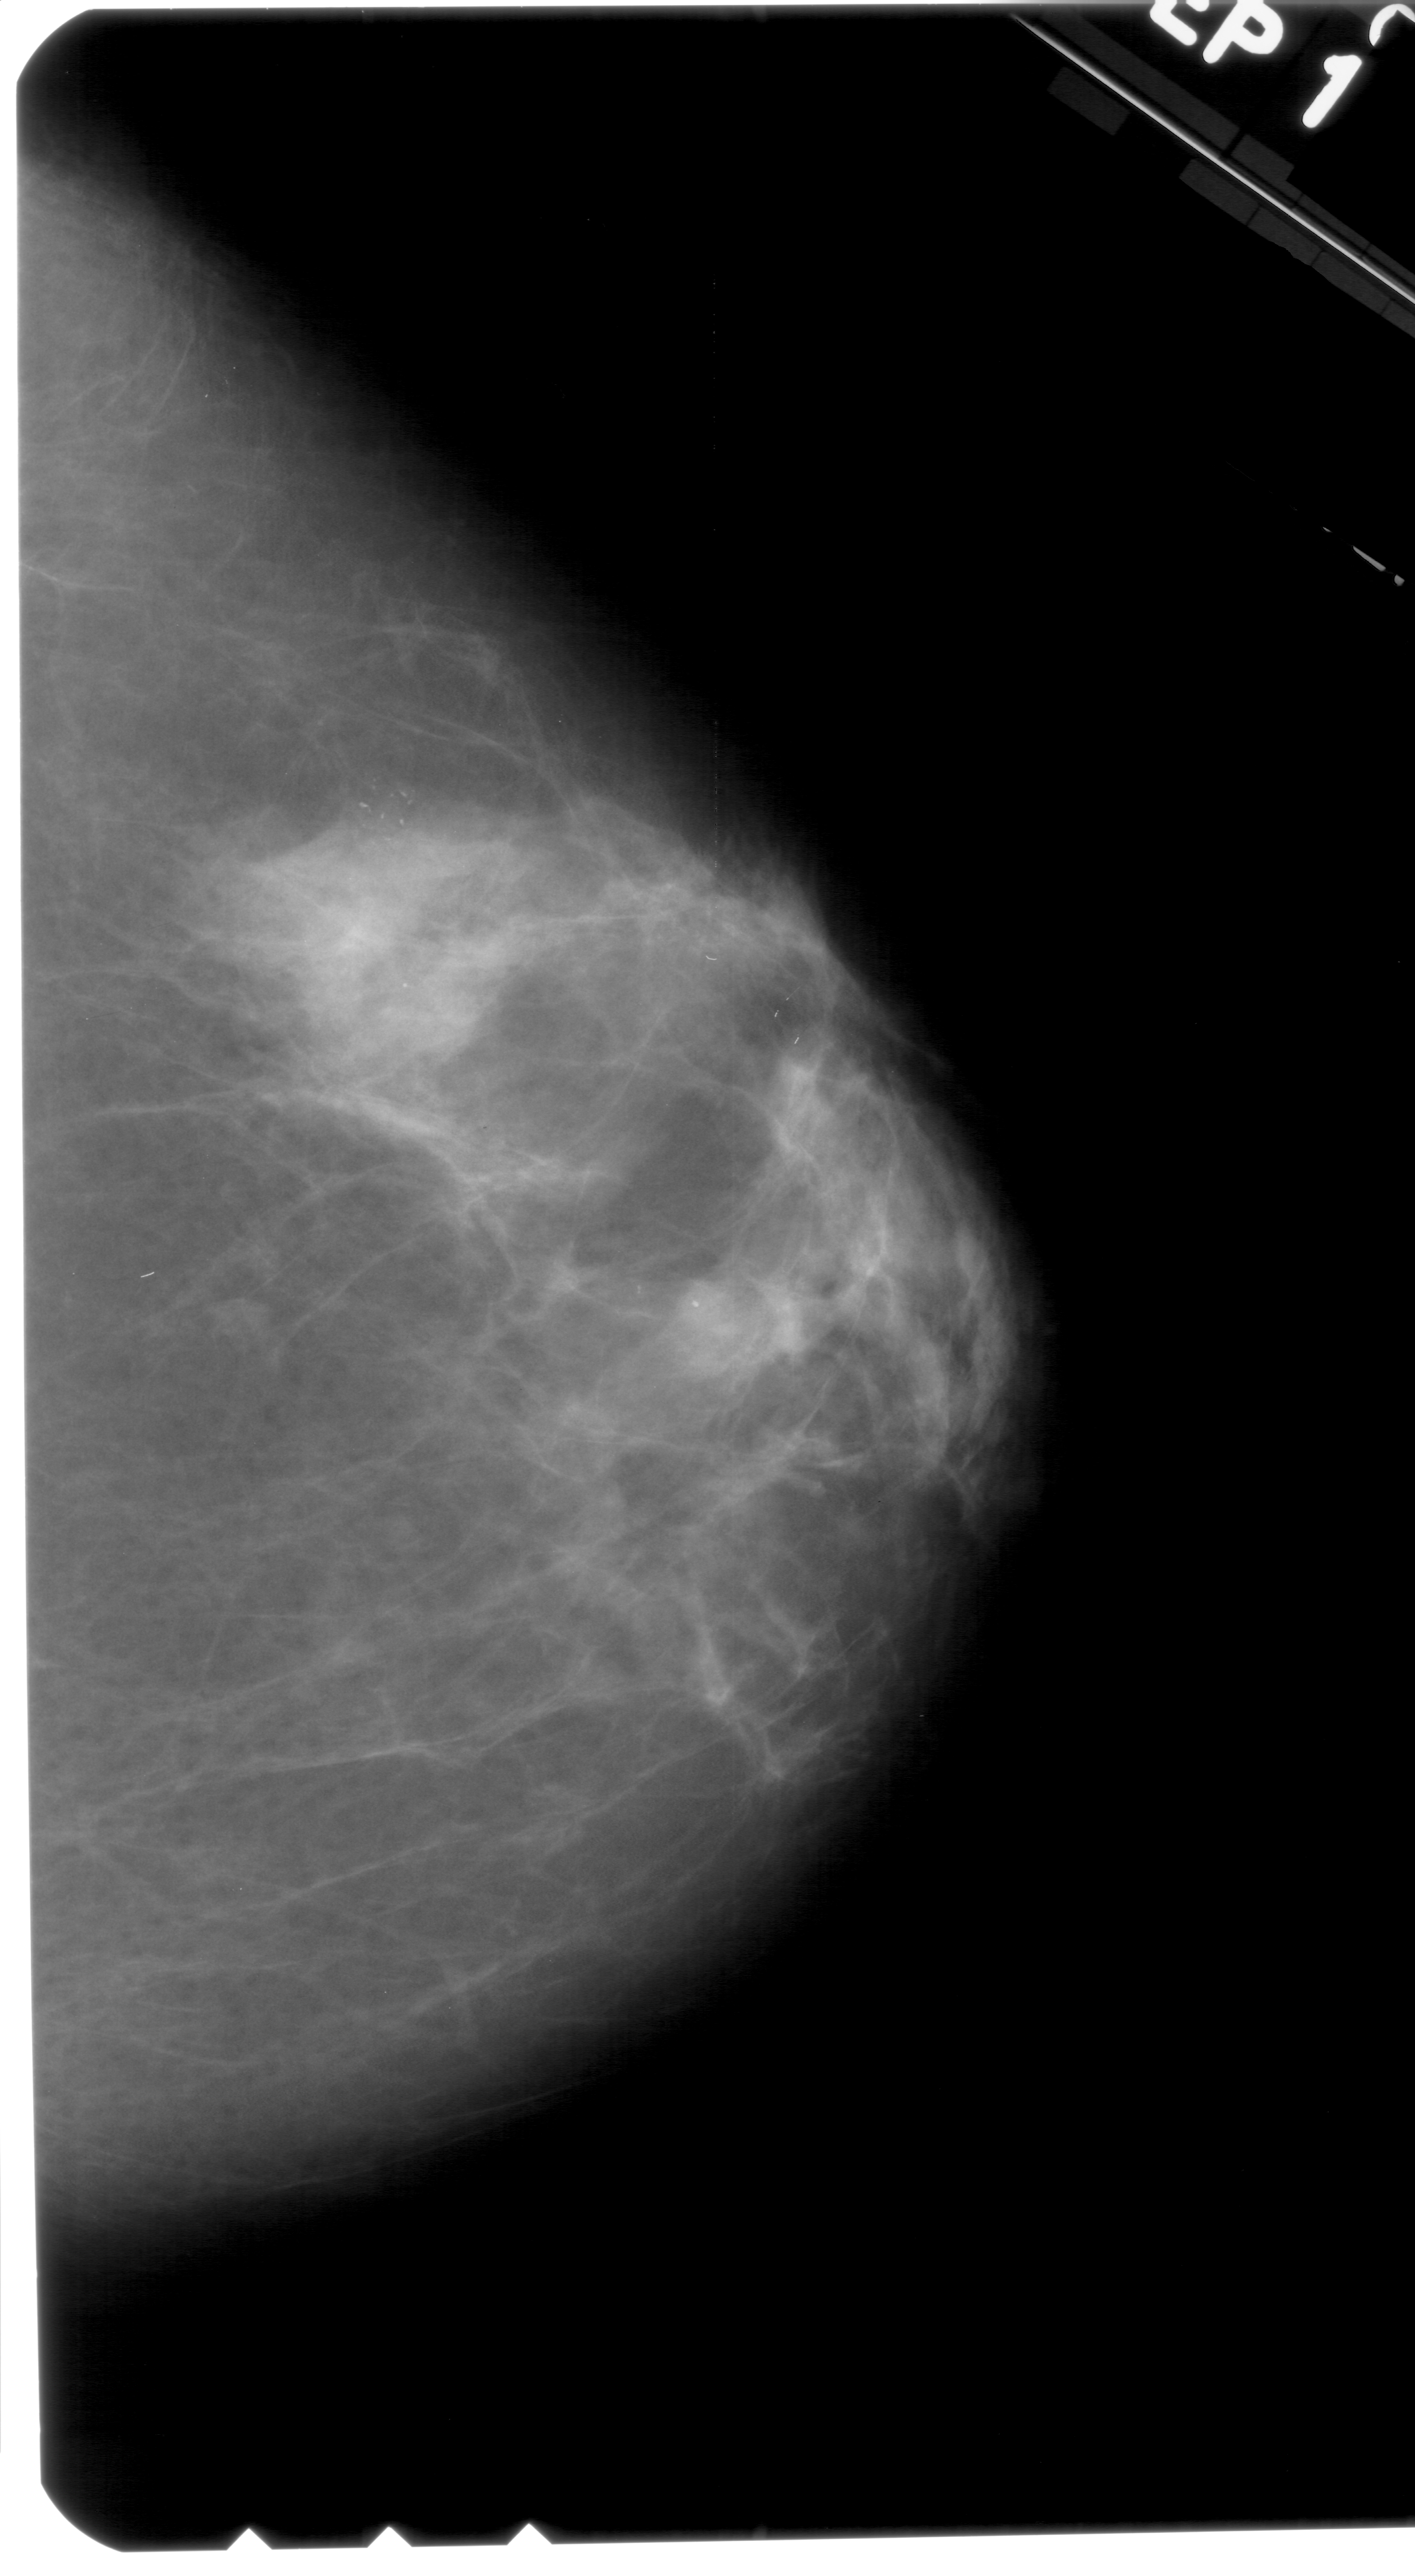
Scanned film-screen mammogram, right breast, CC view, breast composition: extremely dense (BI-RADS density category 4 of 4).
Abnormality record for this image: calcifications, morphology pleomorphic, distribution clustered; BI-RADS assessment category 4; pathology (as recorded): benign.